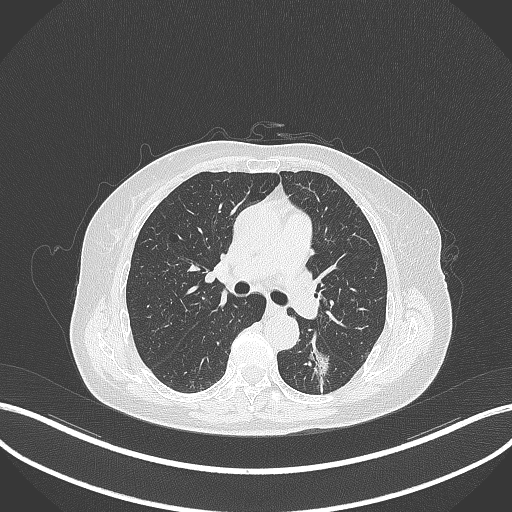
Chest CT, one axial slice. Position 178 of 352 along the scan axis. 120 kVp. Lung window (W 1500 / L -600 HU). 1 mm slice thickness. 512 × 512 image matrix, field of view 400 × 400 mm. Patient: female, 70 years. Case-level facts recorded for this patient, not image findings: clinical TNM (as recorded): T1c N0 M0.
Outlined on this slice (rectangle marked by the reading radiologist):
- lung tumour (recorded histology: adenocarcinoma): bounding box [x1, y1, x2, y2] px = [303, 339, 333, 386]